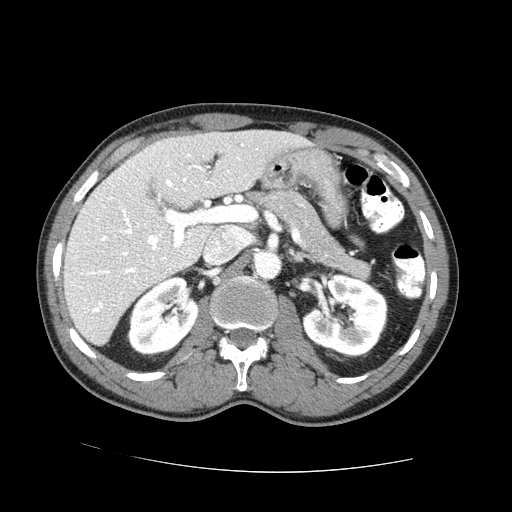
Contrast-enhanced abdominal CT (liver protocol), one axial slice; position 39 of 73 along the scan axis; reconstruction kernel STANDARD; 100 kVp; one of 2 acquisitions stored at this slice position; soft-tissue window (W 400 / L 40 HU); 512 × 512 image matrix. Case-level facts recorded for this patient, not image findings: diagnosis: hepatocellular carcinoma (patient treated with transarterial chemoembolisation; whether this scan precedes or follows treatment is not stated here); TNM stage (as recorded): Stage-IVA; Child-Pugh class: A; tumour differentiation: no biopsy; tumour nodularity: uninodular.
Structures marked on this image (semi-automatically segmented with operator editing):
- liver parenchyma outside the tumour (the mass and vessels are separate outlines, so this box may not span the whole liver): bounding box [x1, y1, x2, y2] px = [64, 130, 309, 344]
- mass: [143, 178, 159, 198]
- liver vessels: [80, 148, 240, 312]